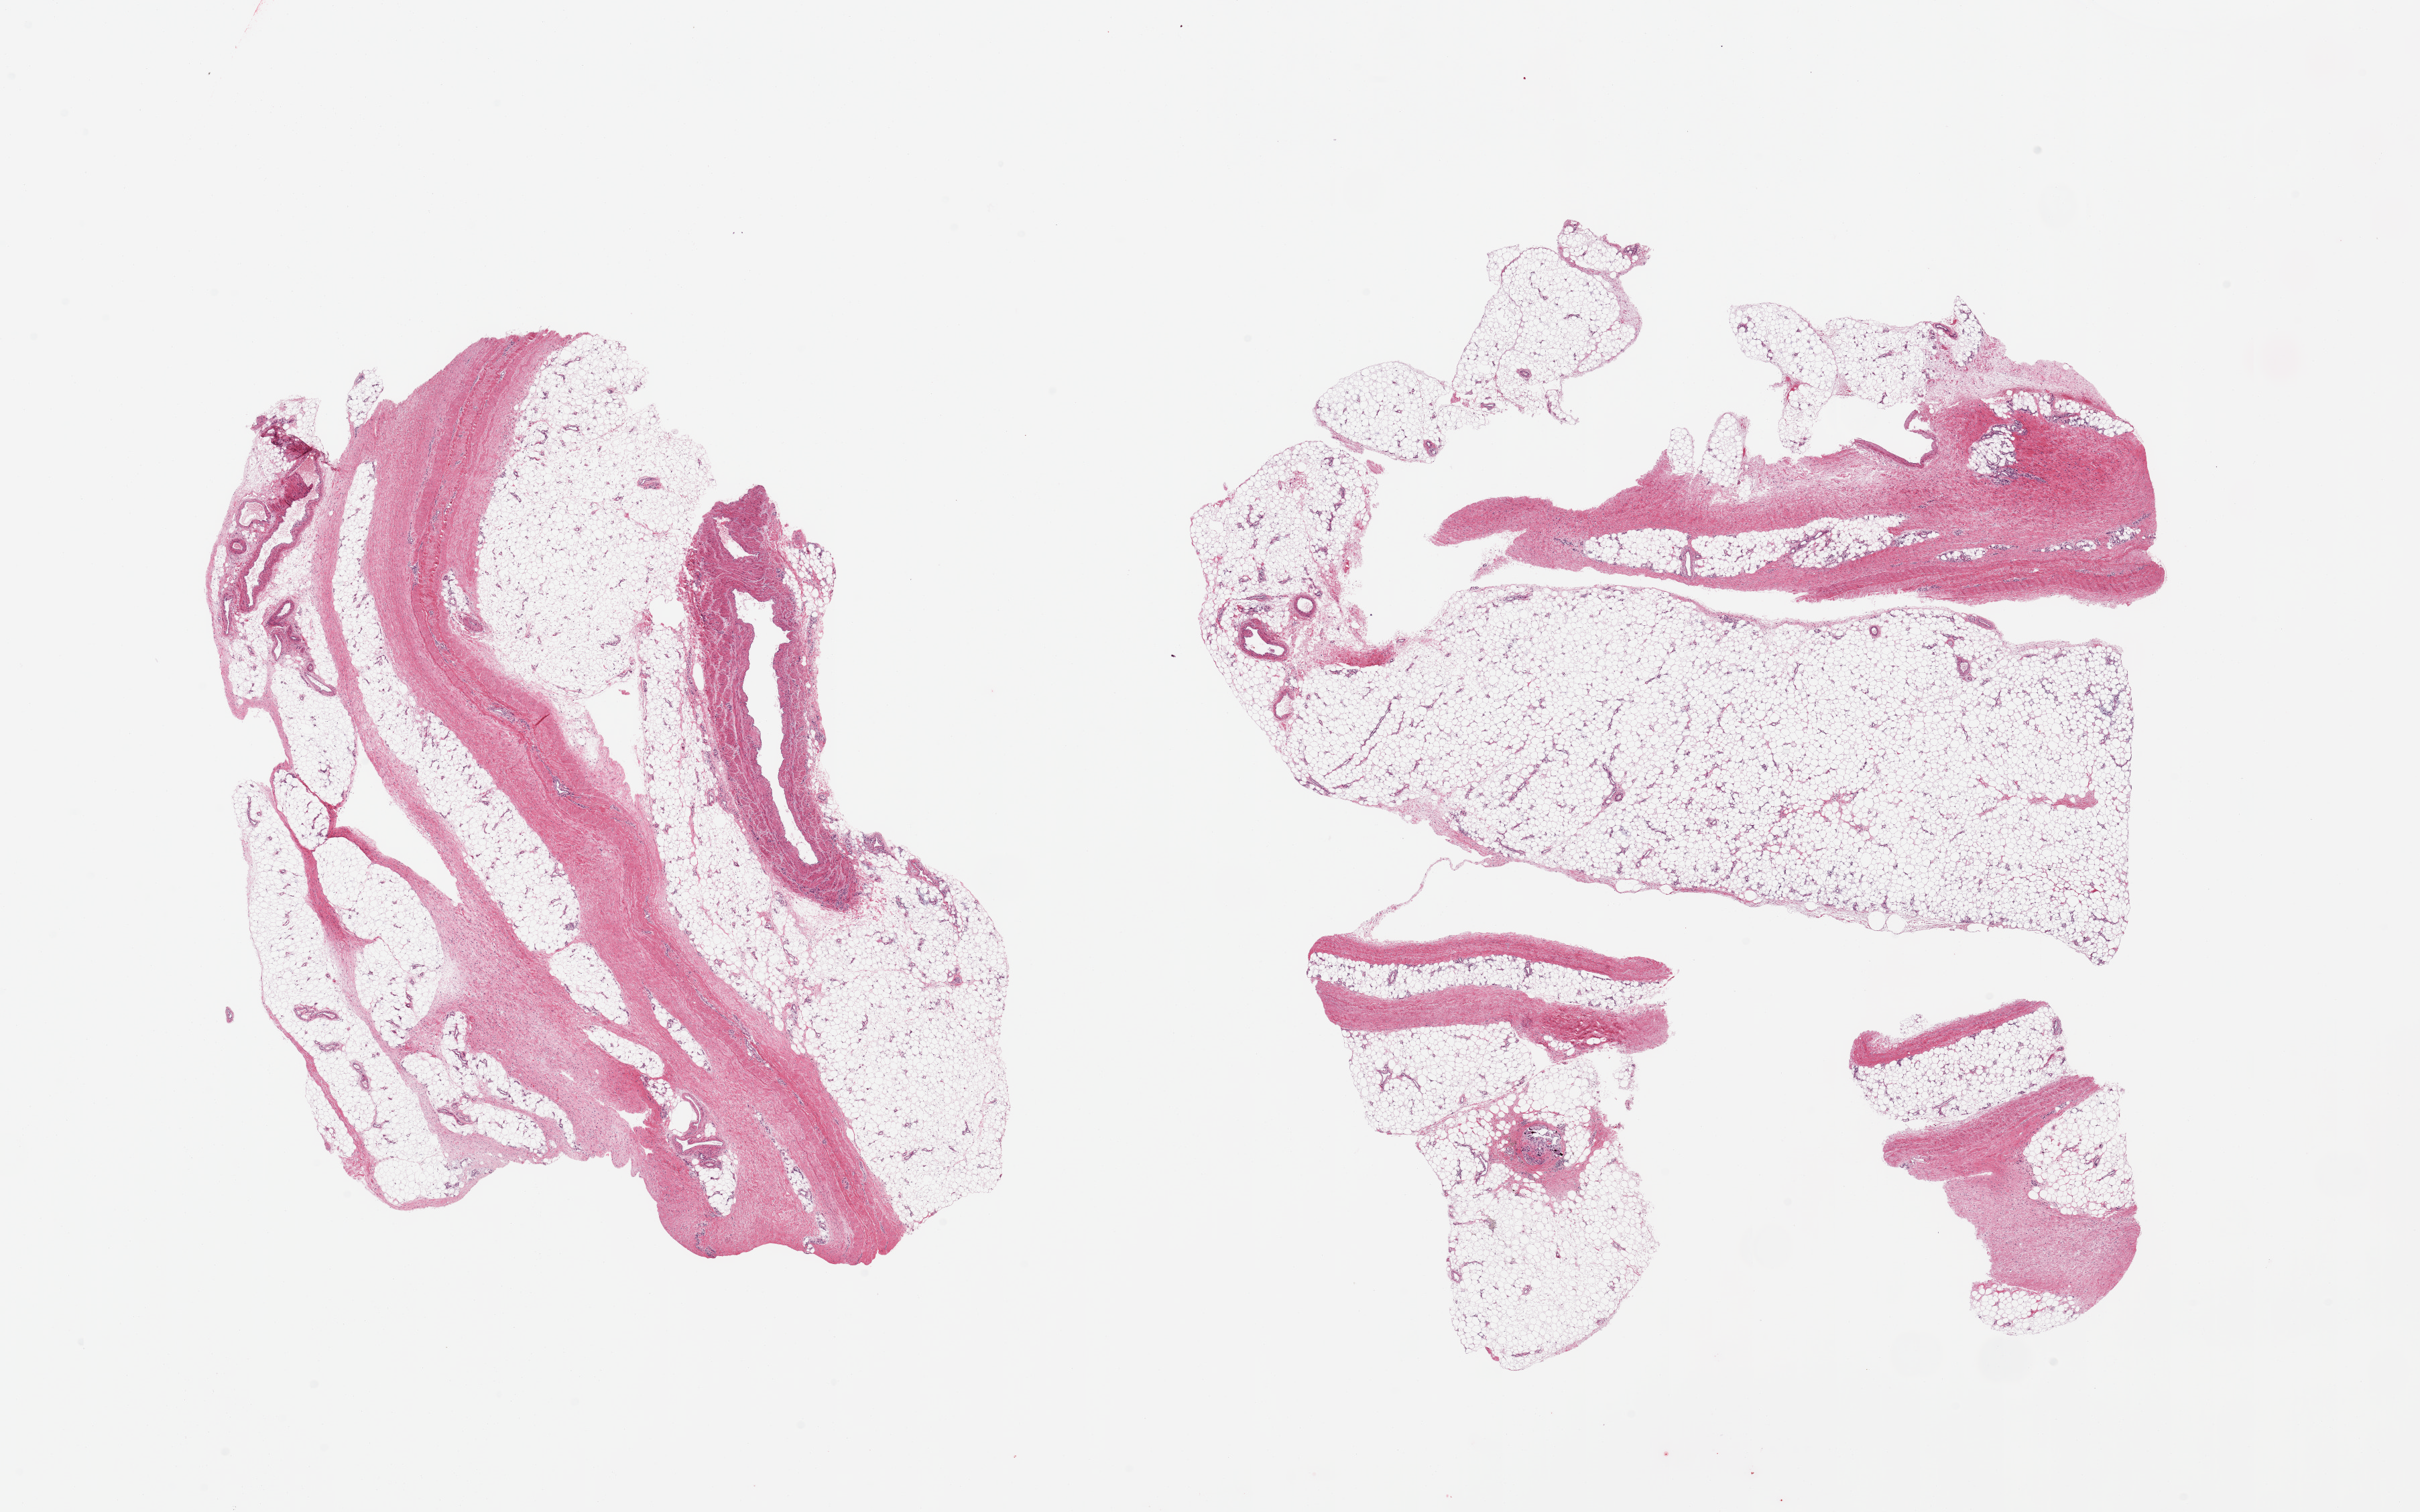
Hematoxylin and eosin (H&E) whole-slide image — low-resolution overview of the scanned area, about 28.5 x 17.8 mm (from a 20x scan); PAXgene-fixed, paraffin-embedded tissue; sampled site (target tissue): adipose tissue; tissue donor sample. Male donor.
Reviewer comment on this tissue sample: 4 pieces; mature adipose tissue with wide fibrous septa (dialysis related nephrogenic fibrosis); prominent vessels; one vessel with recanalization and calcium deposits.